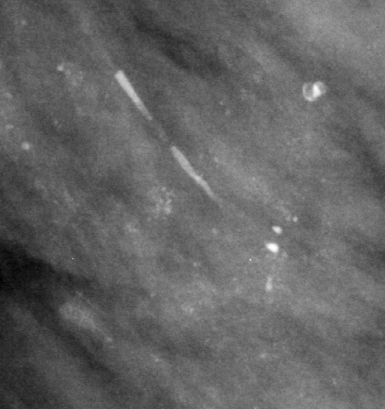
Cropped region of a digitized screen-film mammogram centred on a radiologist-marked abnormality, left breast, MLO view, BI-RADS breast density category 4 (scale 1–4).
Calcifications, morphology punctate / lucent center, distribution regional; BI-RADS assessment category 2; benign without callback (not worked up further).